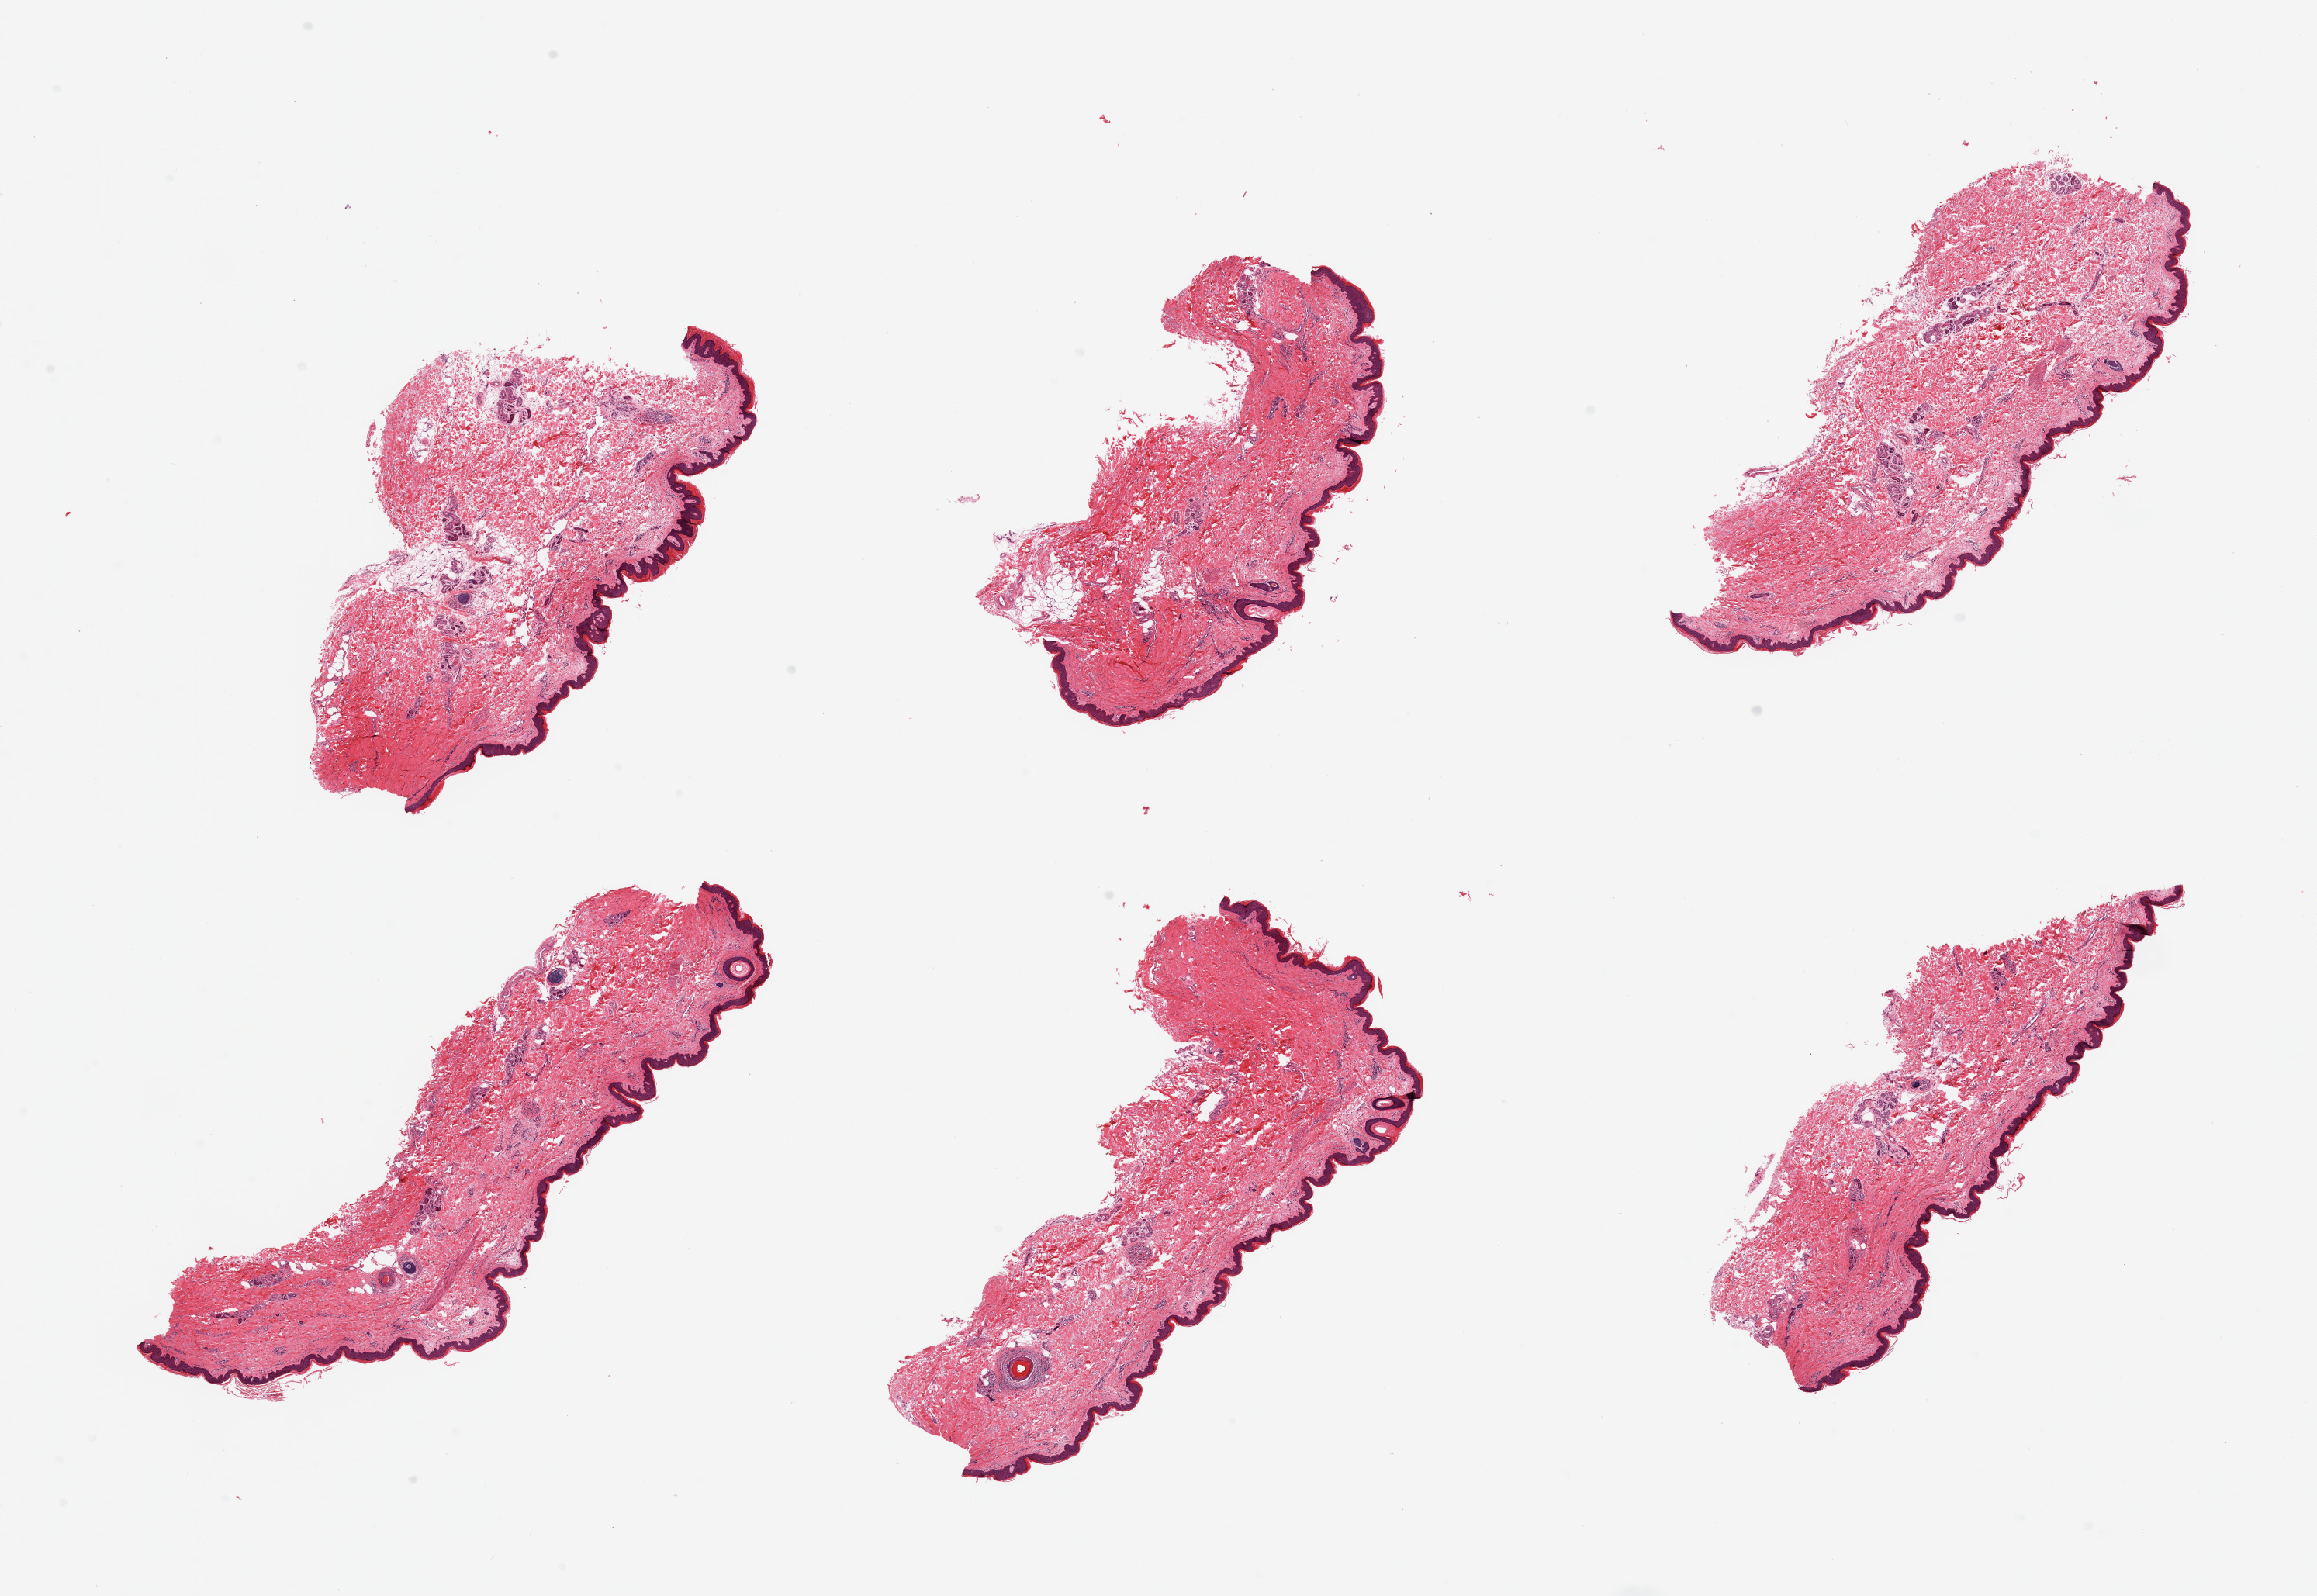
Digitized haematoxylin and eosin-stained section, brightfield — whole scanned area (about 23.6 x 16.3 mm, from a 20x scan) shown as a low-resolution overview. PAXgene-fixed paraffin-embedded (PFPE) section. Sampled site (target tissue): skin of lower leg. Donor tissue sample. Donor sex: male.
Reviewer comment on this tissue sample: 6 pieces; minimal internal fat, epidermis measures 43 microns.